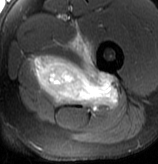
MRI of an extremity soft-tissue mass, one axial slice. Position 57 of 70 along the scan axis. T2-weighted fat-saturated. MR volume resampled by the dataset authors to the PET/CT grid (not the native acquisition matrix). 3.27 mm slice thickness. 158 × 164 image matrix. Male patient. From the clinical record (not read from this slice): histological type: extraskeletal osteosarcoma; grade: high; site of the primary tumour: left adductur.
Annotated regions visible in this slice (expert contour drawn on MRI and transferred to this co-registered scan by the dataset authors):
- gross tumour volume (mass): bounding box <29,34,119,109> (left, top, right, bottom; pixels)